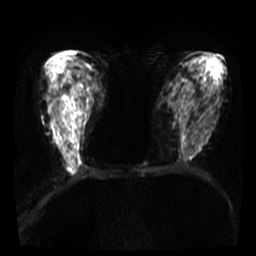
Breast MRI, one axial slice; slice 18 of 36 in the series (ordered by position); diffusion-weighted series; image 2 of 4 stored at this slice position (different b-values; order by instance number); 3 T; 256 × 256 image matrix, field of view 300 × 300 mm. Female patient.
Outlined on this slice (manually delineated by an expert):
- tumour on diffusion-weighted imaging: bounding box [x1, y1, x2, y2] px = [72, 141, 79, 156]